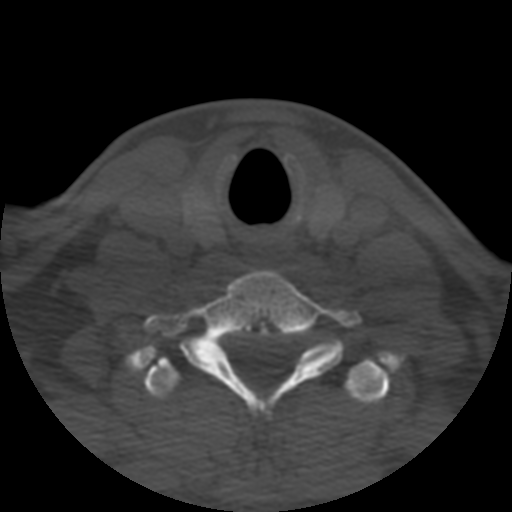
CT including the spine, one axial slice; bone window (W 1800 / L 400 HU); 1.25 mm slice thickness; 512 × 512 image matrix, field of view 160 × 160 mm. Patient age 57 years. From the clinical record (not read from this slice): primary cancer: prostate.
Outlined on this slice (semi-automatically segmented with operator editing):
- T1 vertebra: box from (x=143, y=358) to (x=391, y=404) px